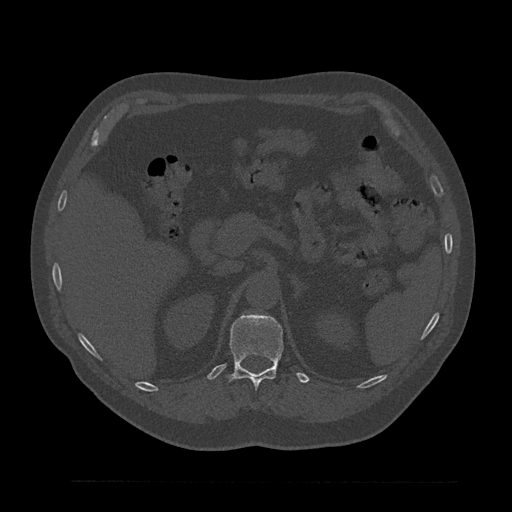
CT including the spine, one axial slice. Position 225 of 797 along the scan axis. Reconstruction kernel Br40s/3. 120 kVp. Bone window (W 1800 / L 400 HU). 0.5 mm slice thickness. 512 × 512 image matrix, field of view 430 × 430 mm. Patient: male, 61 years. Case-level facts recorded for this patient, not image findings: primary cancer: prostate.
Structures marked on this image (semi-automatically segmented with operator editing):
- T12 vertebra: box from (x=228, y=313) to (x=283, y=389) px